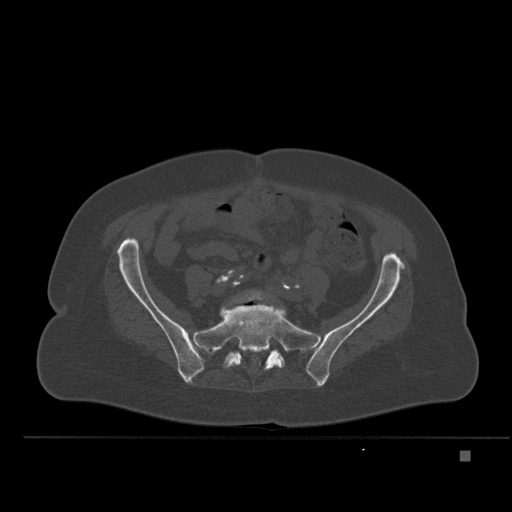
CT including the spine, one axial slice. Position 145 of 477 along the scan axis. Bone window (W 1800 / L 400 HU). 1.5 mm slice thickness. 512 × 512 image matrix, field of view 422 × 422 mm. Female patient, age 74 years. From the clinical record (not read from this slice): primary cancer: colon.
Outlined on this slice (semi-automatically segmented with operator editing):
- L5 vertebra: bounding box <244,290,264,301> (left, top, right, bottom; pixels)